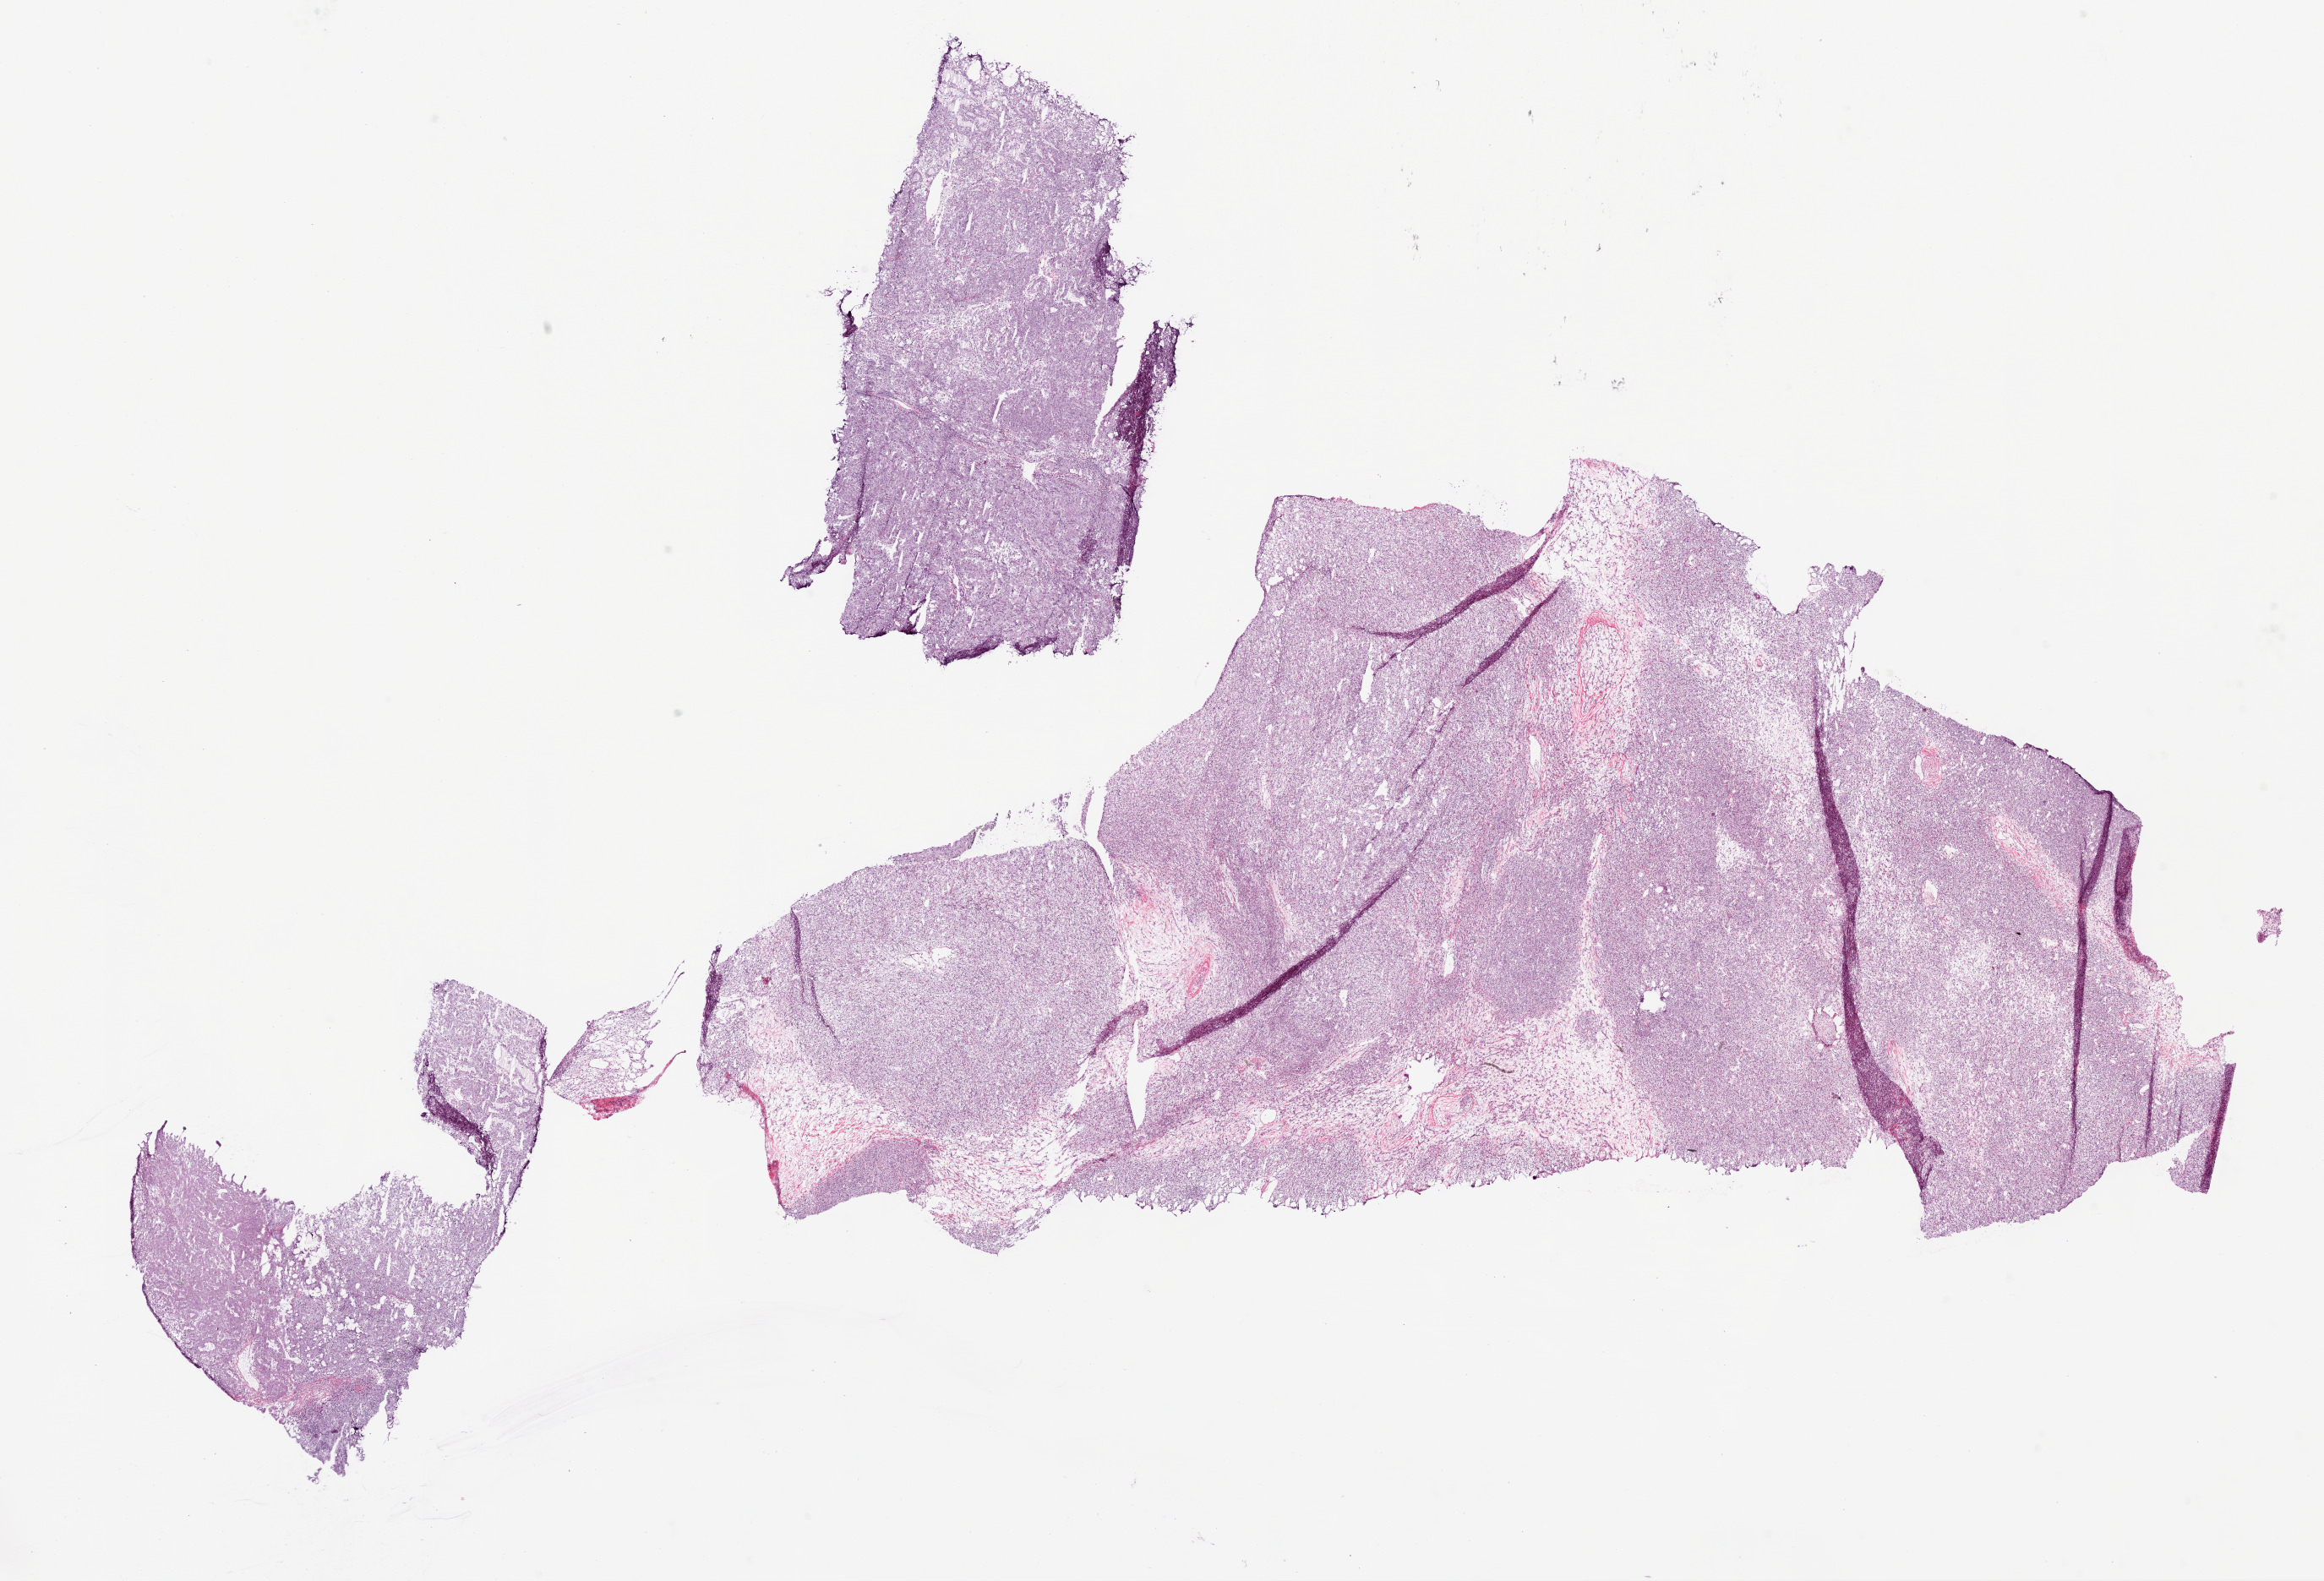
Hematoxylin and eosin (H&E) stained whole-slide image — whole scanned area (about 22.1 x 15.0 mm, slide scanned at 20x) shown as a low-resolution overview, frozen section from the bottom of the tissue portion, primary tumour sample from the kidney. Patient: male, age at initial diagnosis 52 years. Histologic grade: G3 (poorly differentiated). Pathologist review of this section (percent, as recorded): tumour cells 100%, tumour nuclei 88%, normal cells 0%, stromal cells 0%, necrosis 0%. Infiltration values recorded for this section: lymphocyte infiltration 2%.
• diagnosis: Clear cell adenocarcinoma, NOS
• AJCC pathologic stage: II